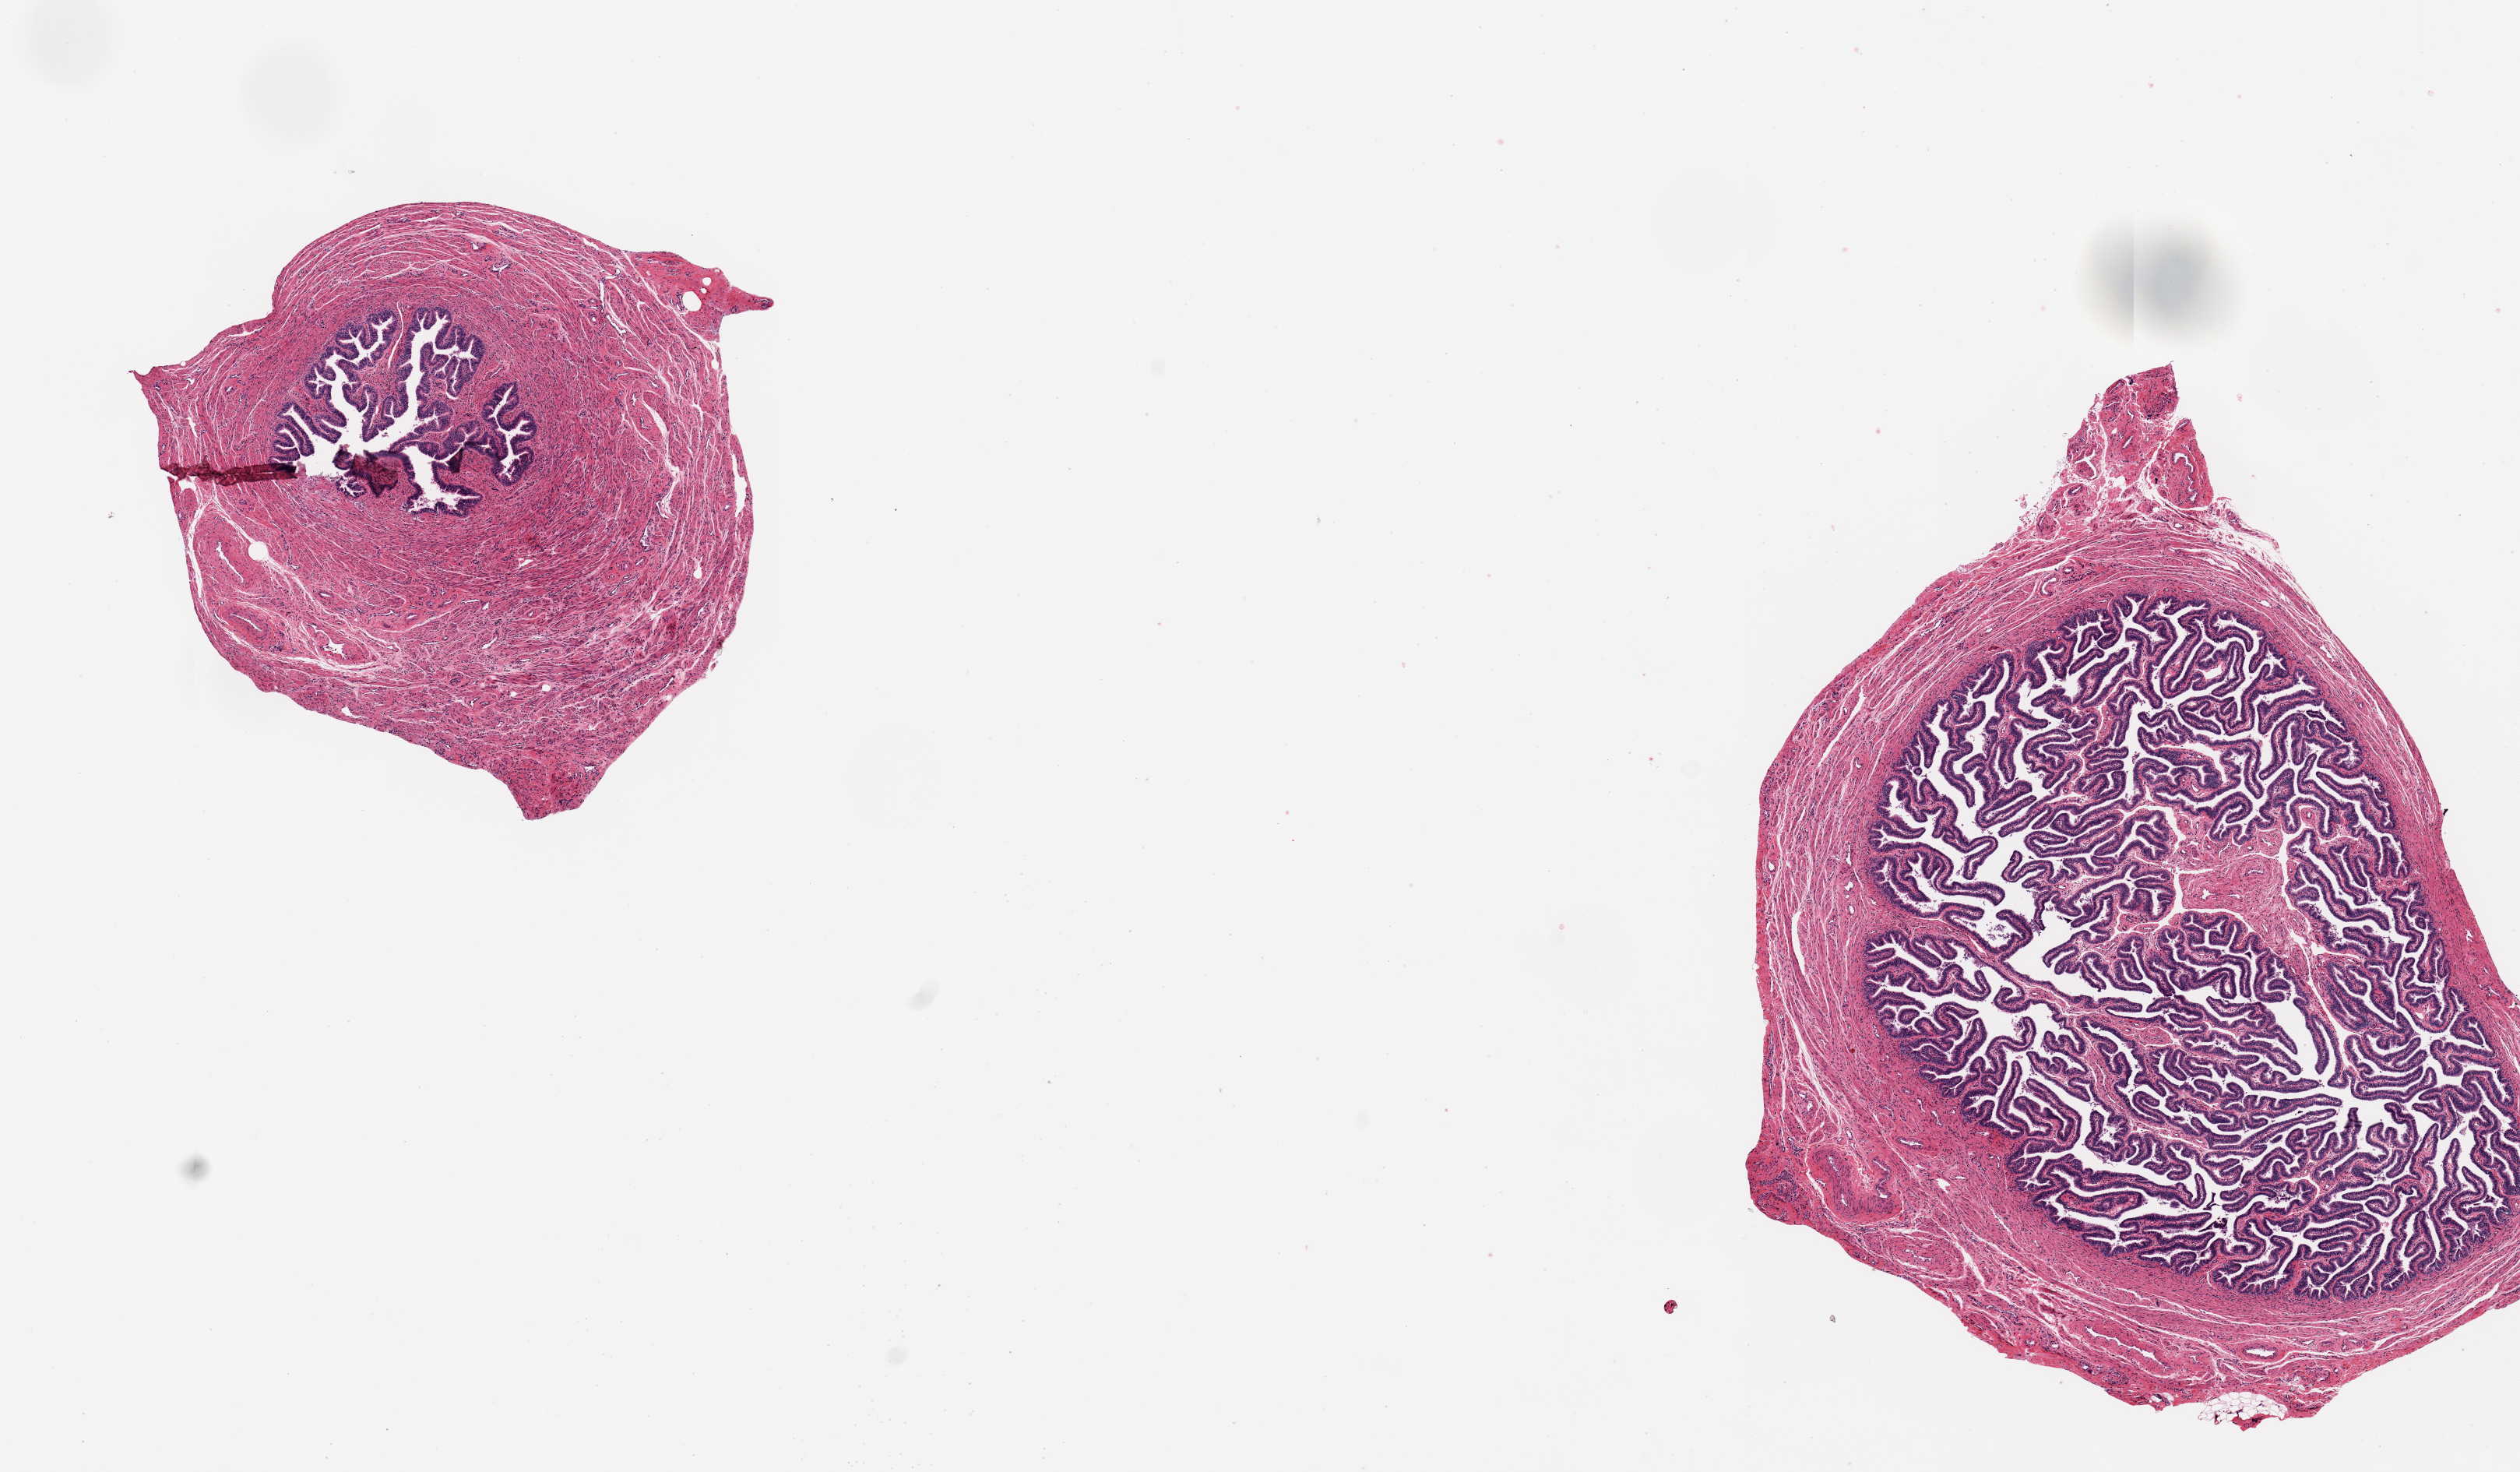
Whole-slide image, hematoxylin and eosin (H&E) stain, brightfield, low-resolution overview of the scanned area, about 12.8 x 7.5 mm (slide scanned at 20x). PAXgene-fixed, paraffin-embedded tissue. Sampled site (target tissue): fallopian tube. Donor tissue sample. Female donor.
* pathologist's review note for this sample: 2 pieces, 4.5x4 mm, 3x3mm; well preserved and cut